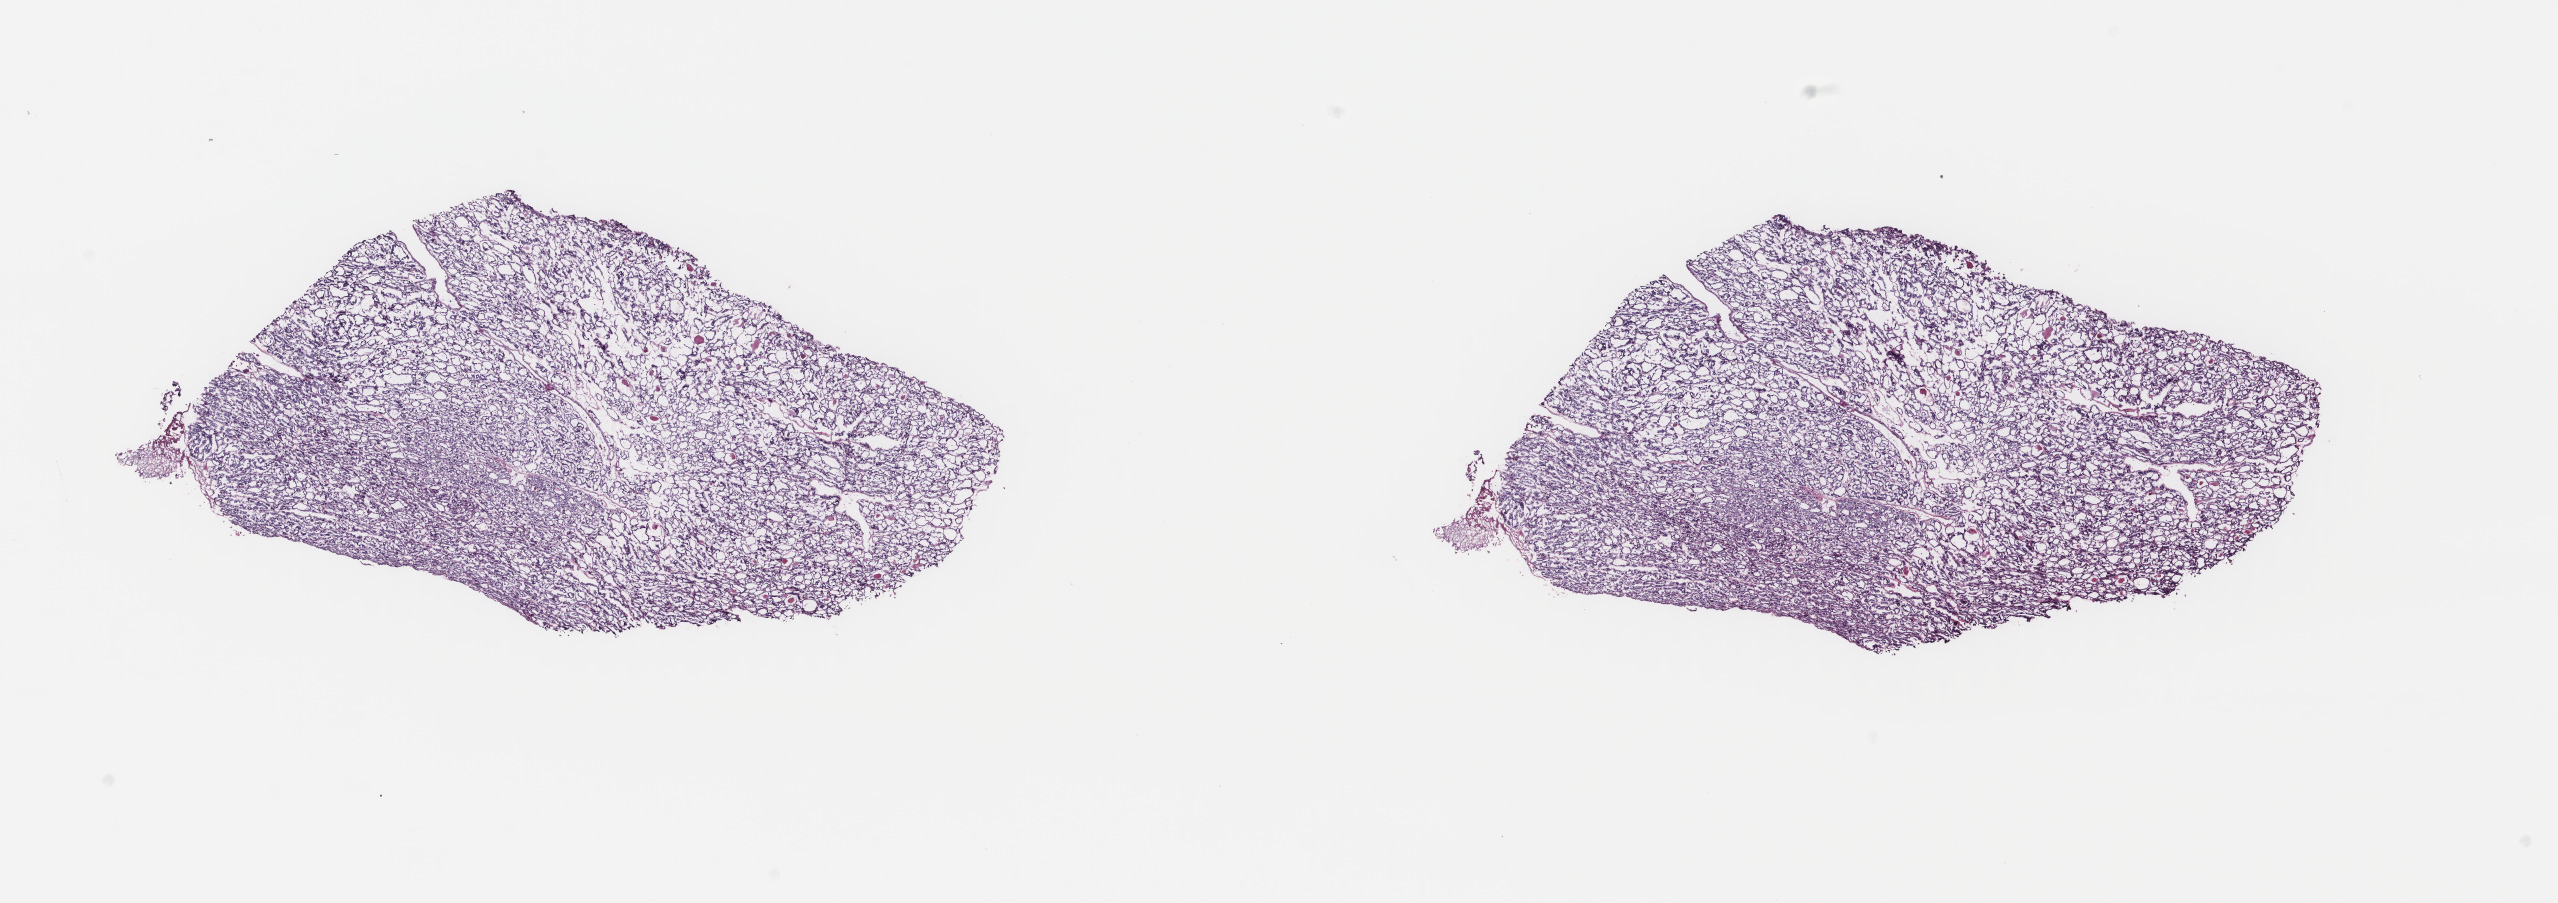
H&E whole-slide image — low-resolution overview of the scanned area, about 20.3 x 7.2 mm; frozen section; primary tumour sample from the thyroid. Female, age 20 years at initial diagnosis. Composition of this section per pathologist review: tumour cells 100%, tumour nuclei 95%, normal cells 0%, stromal cells 0%, necrosis 0%. Infiltration values recorded for this section: lymphocyte infiltration 0%, monocyte infiltration 0%, neutrophil infiltration 0%.
* TNM: T3 N0 MX
* lymph nodes positive (case pathology): 0 of 4 examined
* pathologic diagnosis: Papillary adenocarcinoma, NOS
* laterality: left
* AJCC pathologic stage: I (6th edition)